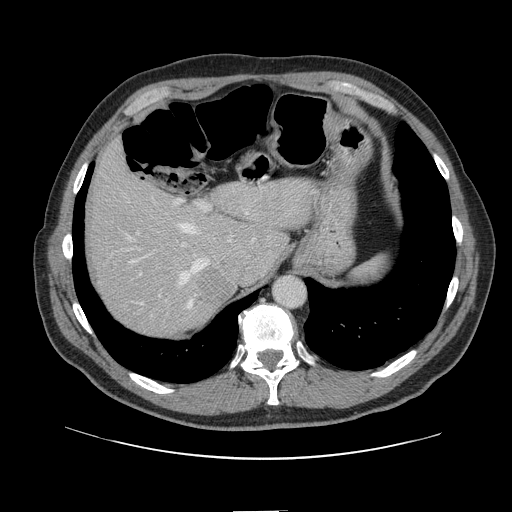
Contrast-enhanced abdominal CT, one axial slice. Intravenous contrast given. Soft-tissue window (W 400 / L 40 HU). 512 × 512 image matrix, field of view 412 × 412 mm. Male patient, age 66 years. From the clinical record (not read from this slice): diagnosis: colorectal cancer liver metastases, imaged before liver resection; multiple liver metastases: no.
Outlined on this slice (manually delineated by an expert):
- hepatic veins: box from (x=127, y=210) to (x=248, y=310) px
- liver: (x=90, y=146)–(x=312, y=335)
- planned liver remnant (the part of the liver to remain after resection): (x=90, y=146)–(x=312, y=307)
- portal vein (with intrahepatic branches): (x=121, y=199)–(x=211, y=298)
- liver metastasis: (x=199, y=270)–(x=234, y=306)